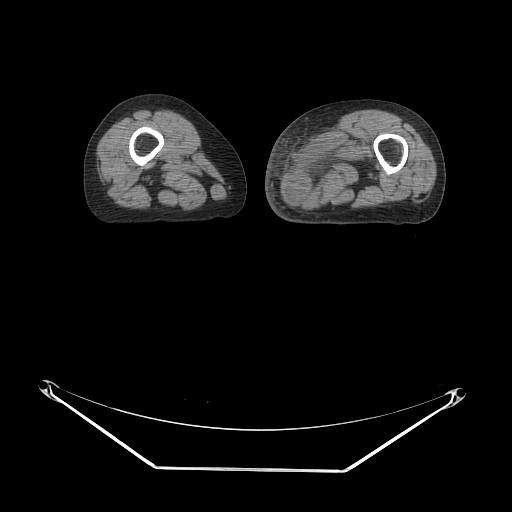
CT of an extremity soft-tissue mass (from a PET/CT study), one axial slice; position 17 of 91 along the scan axis; 140 kVp; soft-tissue window (W 400 / L 40 HU); 3.75 mm slice thickness; 512 × 512 image matrix, field of view 500 × 500 mm. Female patient. Case-level facts recorded for this patient, not image findings: histological type: pleomorphic leiomyosarcoma; grade: high; site of the primary tumour: left thigh.
Structures marked on this image (expert contour drawn on MRI and transferred to this co-registered scan by the dataset authors):
- gross tumour volume including surrounding oedema: box from (x=286, y=130) to (x=373, y=204) px
- gross tumour volume (mass): (x=288, y=162)–(x=323, y=202)